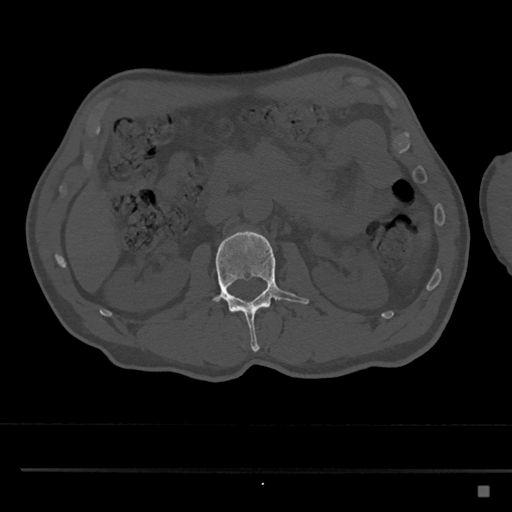
CT including the spine, one axial slice. Position 758 of 797 along the scan axis. Reconstruction kernel Br40s/3. Bone window (W 1800 / L 400 HU). 0.5 mm slice thickness. 512 × 512 image matrix. Male patient, age 59 years. From the clinical record (not read from this slice): primary cancer: prostate.
Outlined on this slice (semi-automatically segmented with operator editing):
- L2 vertebra: bounding box (x1, y1, x2, y2) in pixels: (213, 230, 309, 352)